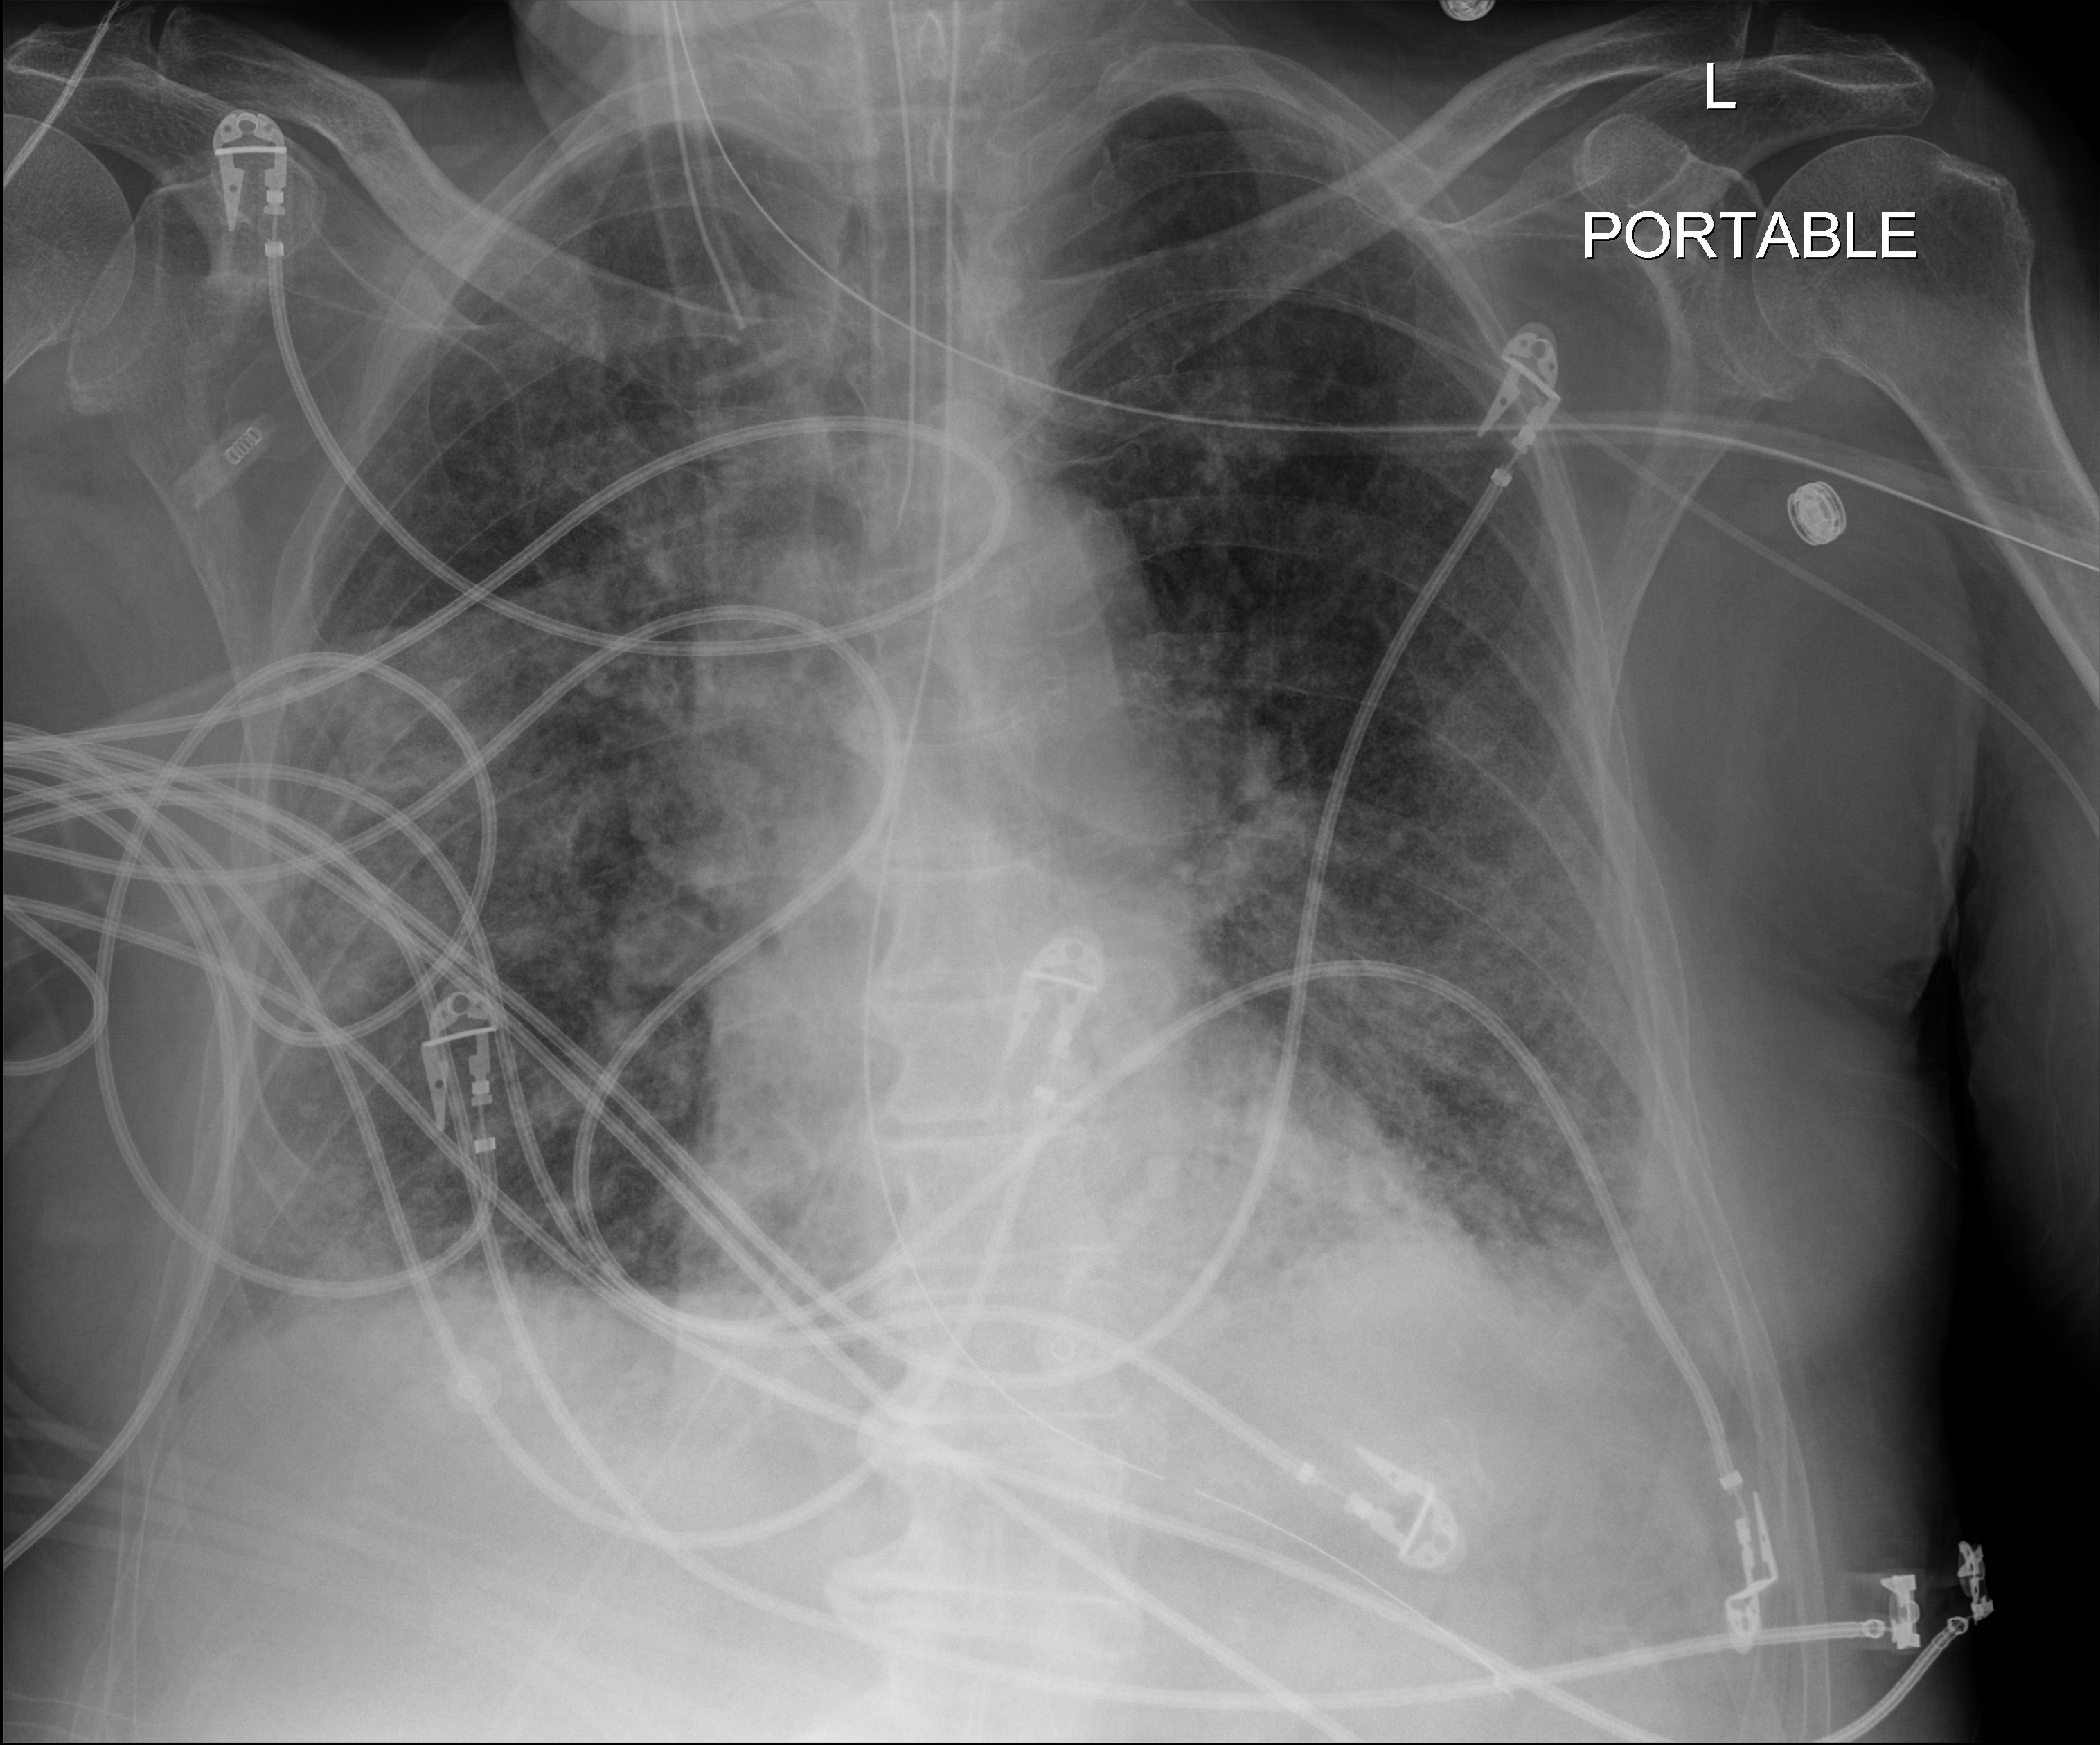
Chest X-ray (portable), anteroposterior (AP) projection. Patient hospitalised with COVID-19; male, aged 75–90 years.
From the hospital-stay record, not from the radiograph (when in the stay this image was taken is not recorded): admitted to intensive care during this hospital stay: yes.